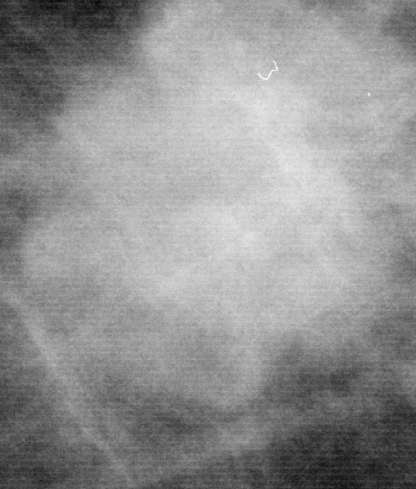
Crop from a digitized film mammogram around one marked abnormality, left breast, CC view.
- Marked abnormality: mass, shape lobulated, margins microlobulated; BI-RADS assessment category 5; pathology (as recorded): malignant.